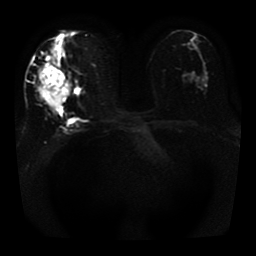
Breast MRI, one axial slice. Position 20 of 41 along the scan axis. Diffusion-weighted series; image 2 of 4 stored at this slice position (different b-values; order by instance number). 1.5 T. 5 mm slice thickness. 256 × 256 image matrix, field of view 330 × 330 mm. Female patient.
Outlined on this slice (outlined manually by an expert reader):
- tumour on diffusion-weighted imaging: bounding box <38,54,70,107> (left, top, right, bottom; pixels)